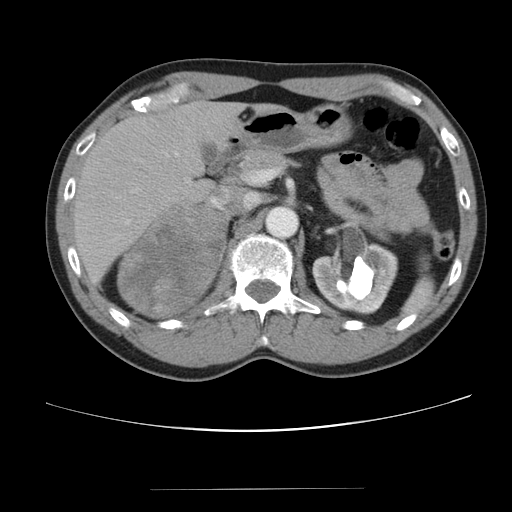
Contrast-enhanced abdominal CT, one axial slice. Position 62 of 80 along the scan axis. 120 kVp. Intravenous contrast given. Soft-tissue window (W 400 / L 40 HU). 5 mm slice thickness. 512 × 512 image matrix. Male patient, age 61 years. From the clinical record (not read from this slice): diagnosis: adrenocortical carcinoma; tumour side: right adrenal; tumour size at pathology: 11.1 cm; Ki-67 index: 32 %; stage (as recorded): 2.
Structures marked on this image (semi-automatic segmentation, software-assisted and operator-edited):
- mass: bounding box [x1, y1, x2, y2] px = [119, 206, 224, 316]